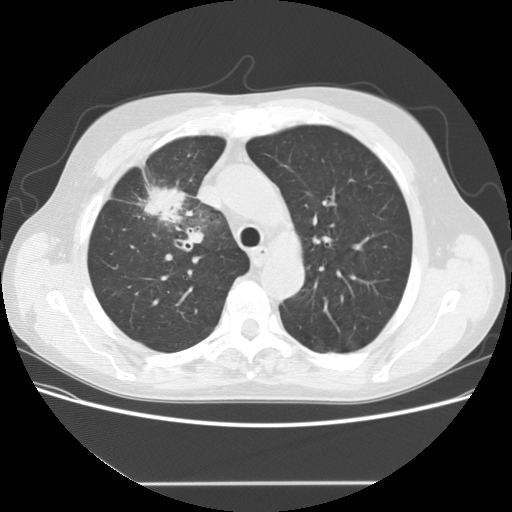
Low-dose screening chest CT, one axial slice; slice 112 of 153 in the series (ordered by position); 120 kVp; lung window (W 1500 / L -600 HU); 2.5 mm slice thickness; 512 × 512 image matrix, field of view 360 × 360 mm.
Annotated regions visible in this slice (expert manual segmentation):
- lesion 1 (tumor, upper lobe of right lung): box from (x=142, y=186) to (x=193, y=224) px